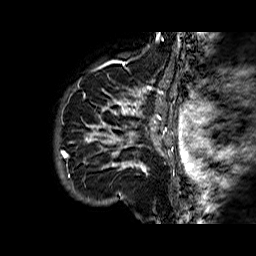
Breast MRI (dynamic contrast-enhanced), one sagittal slice. Slice 54 of 60 in the series (ordered by position). Dynamic contrast-enhanced series, time point 2 of 6 at this slice position (early post-contrast). 1.5 T. TE 6.3 ms, TR 32.4 ms. 256 × 256 image matrix. Female patient. Case-level facts recorded for this patient, not image findings: setting: breast cancer imaged before/during neoadjuvant chemotherapy; receptor status: HR-positive, HER2-negative.
Annotated regions visible in this slice (semi-automatic segmentation, software-assisted and operator-edited):
- analysis volume of interest (the breast-tissue region the enhancement analysis was run in; not a lesion): bounding box <68,72,177,183> (left, top, right, bottom; pixels)
- tumour enhancement mask (voxels above the 100 % enhancement threshold inside the analysis volume of interest): <68,87,174,177>